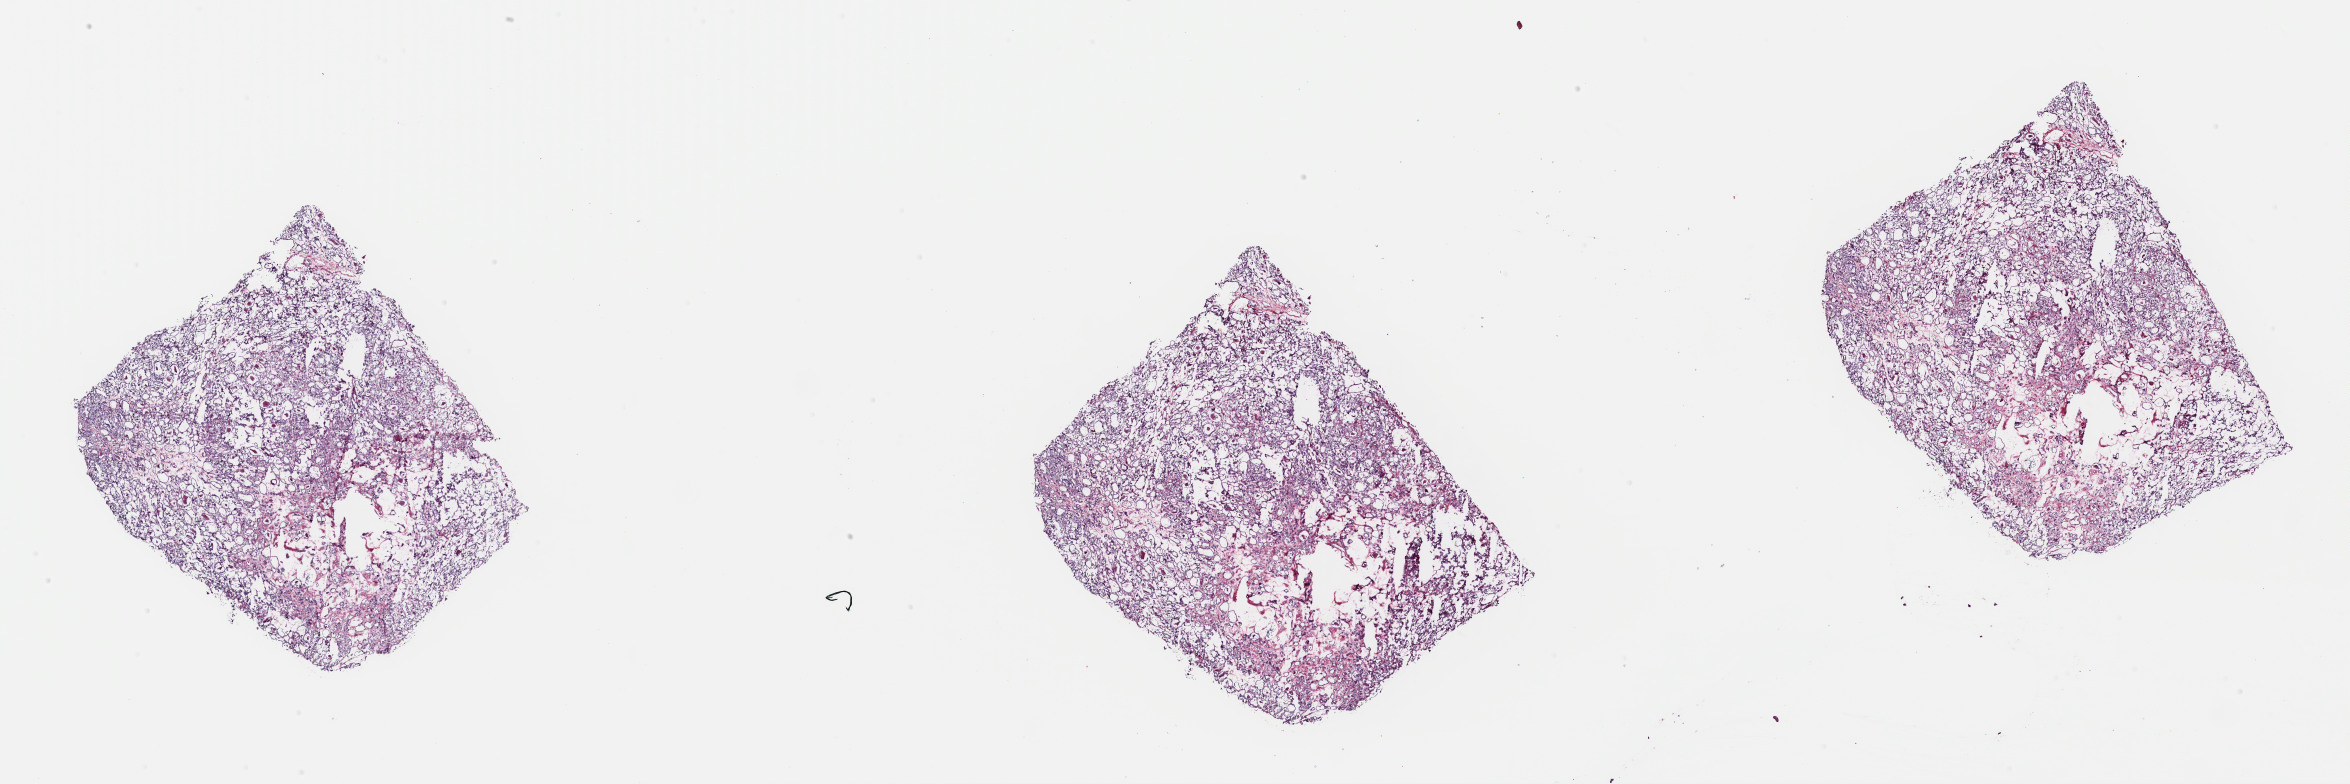
Digitized H&E tissue section (whole slide), whole scanned area (about 37.1 x 12.4 mm, from a 40x scan) shown as a low-resolution overview; frozen section from the top of the tissue portion; primary tumour sample from the thyroid. Patient: male, age at initial diagnosis 33 years. Pathologist review of this section (percent, as recorded): tumour cells 100%, tumour nuclei 80%, normal cells 0%, stromal cells 0%, necrosis 0%. Inflammatory infiltration, as recorded: lymphocyte infiltration 1%, monocyte infiltration 1%, neutrophil infiltration 0%.
- TNM: T2 N0 M0
- pathologic diagnosis: Papillary carcinoma, follicular variant (thyroid gland)
- AJCC pathologic stage: I (7th edition)
- lymph nodes positive (case pathology): 0 of 8 examined